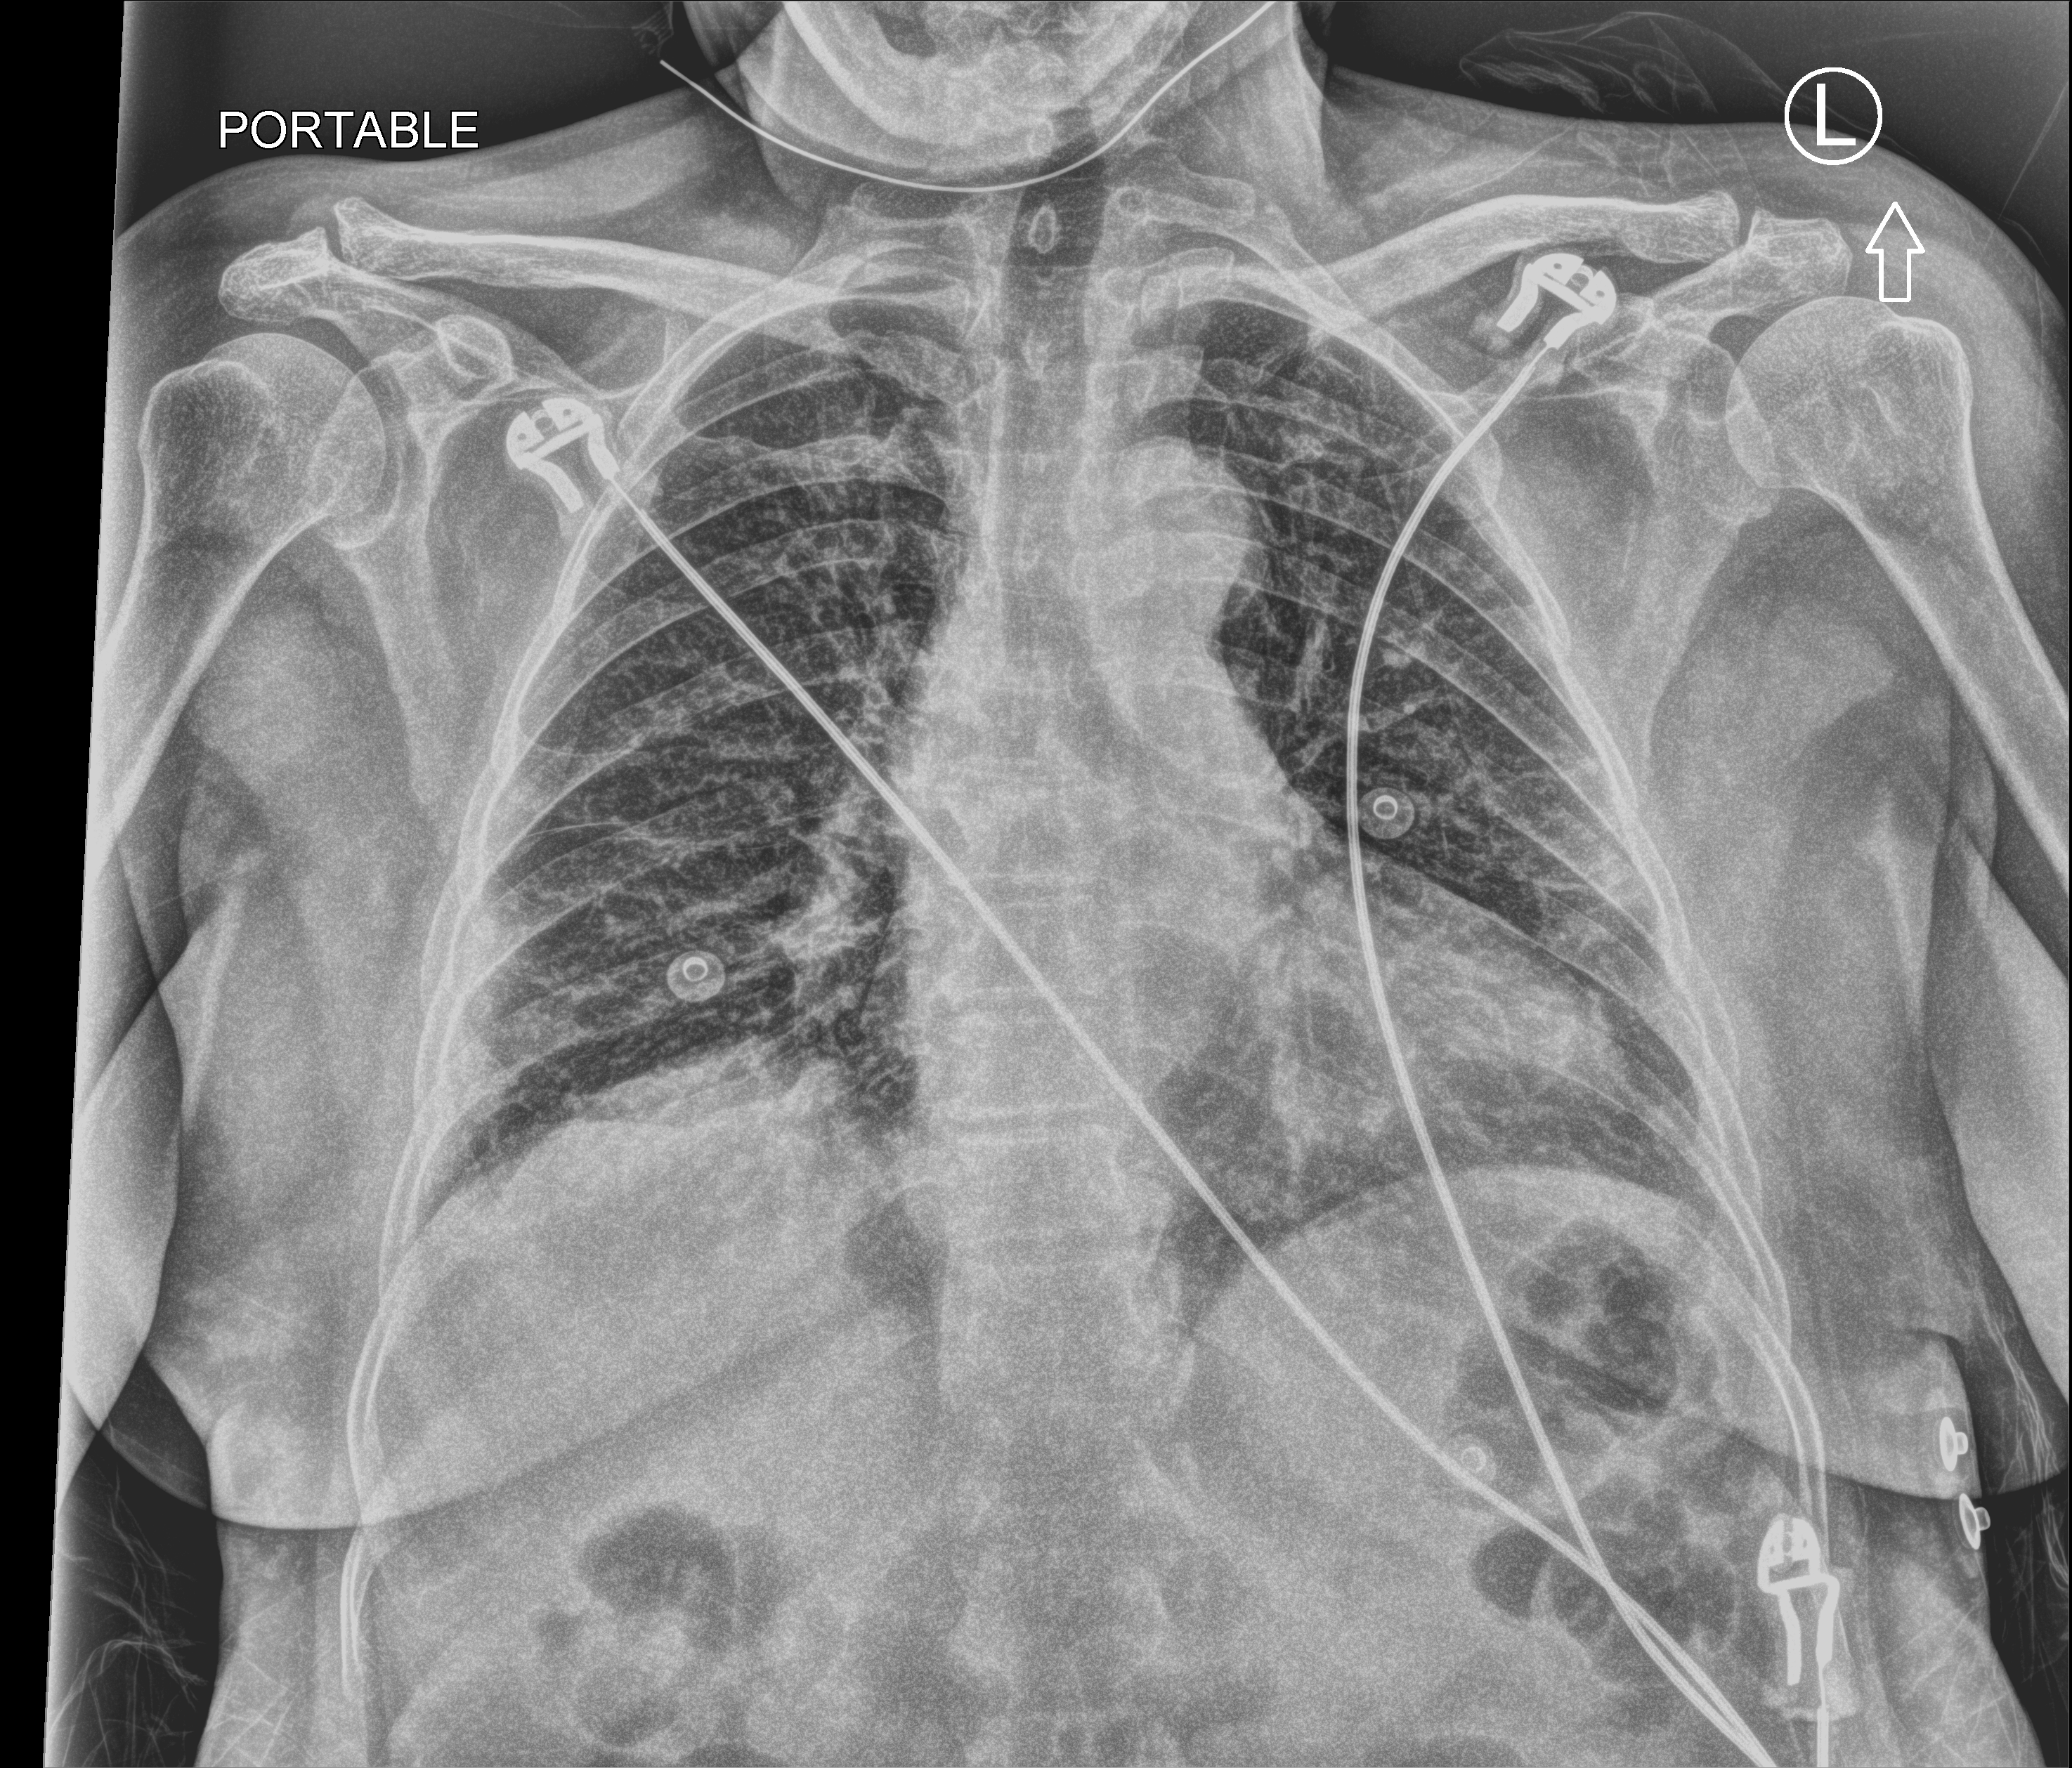
Chest X-ray (portable), anteroposterior (AP) projection. Female patient hospitalised with COVID-19, age 60–74 years.
Hospital-stay facts (about this admission, not read from this image; timing relative to this image not recorded): other chronic lung disease (admission record): no; mechanically ventilated during this hospital stay: no.